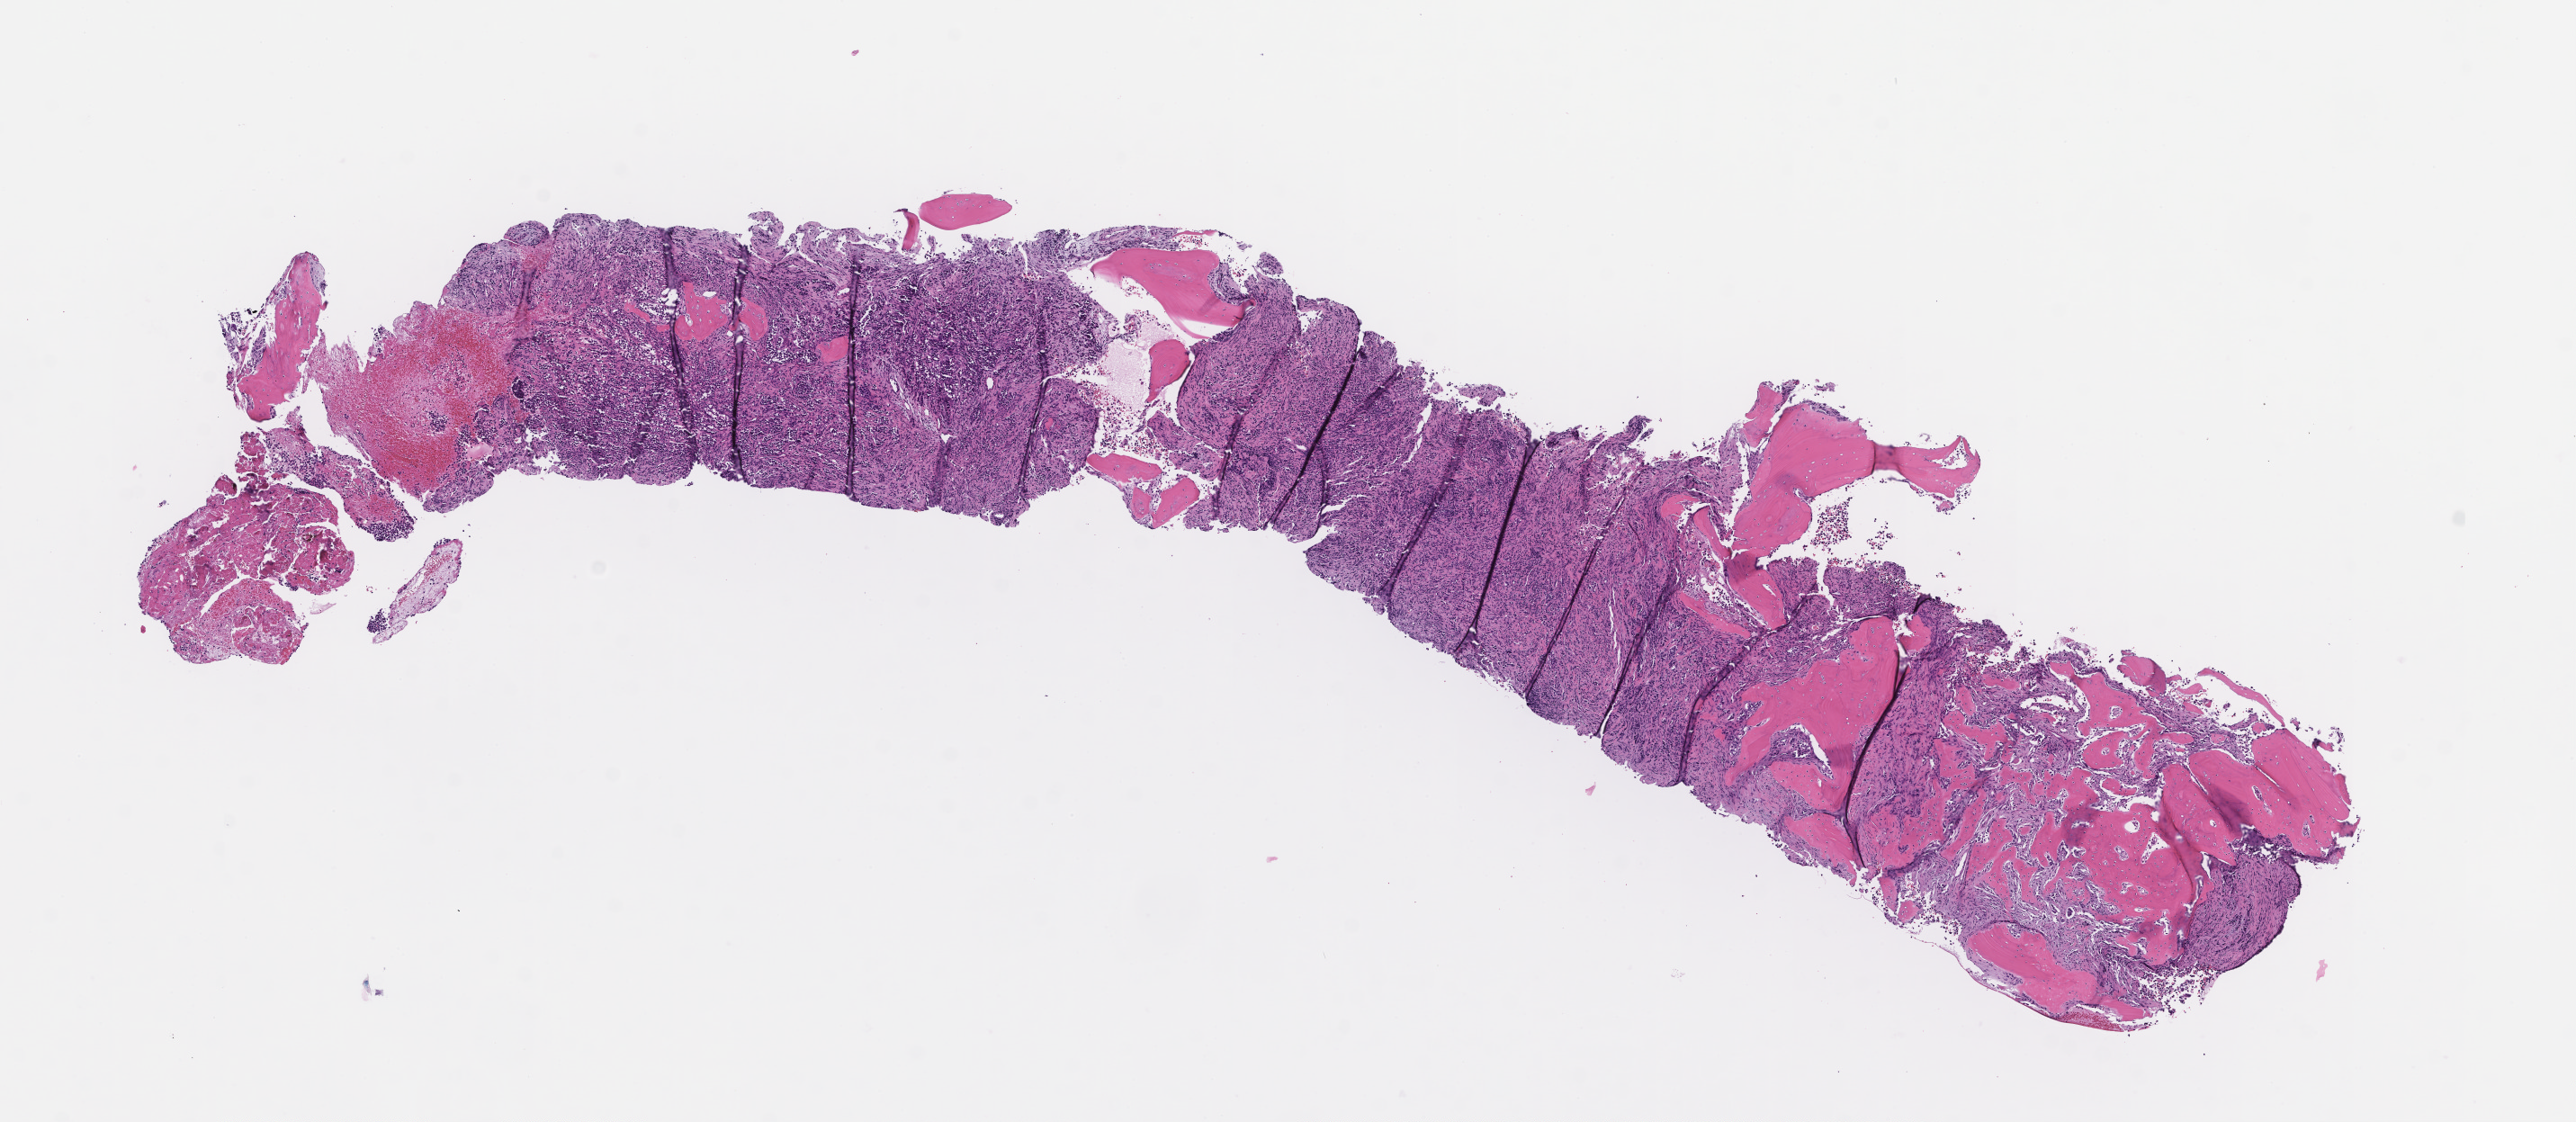
Haematoxylin and eosin whole-slide image — shown as a low-resolution overview of the whole scanned area (about 11.6 x 5.0 mm); formalin-fixed paraffin-embedded section; archival tissue. Patient sex: female.
This section: metastasis (sampled organ not recorded). Primary diagnosis of the patient: Invasive Breast Carcinoma.